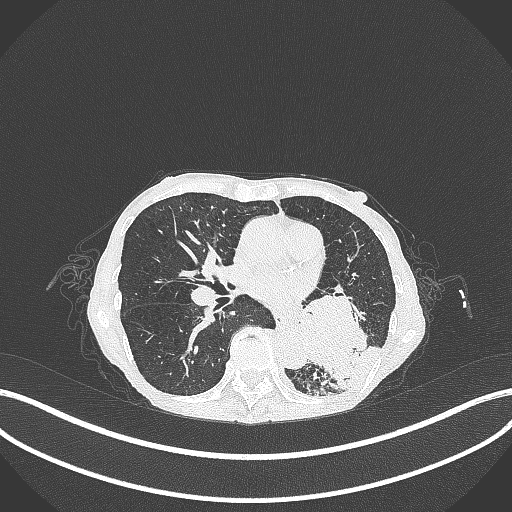
Chest CT, one axial slice; position 133 of 347 along the scan axis; lung window (W 1500 / L -600 HU); 512 × 512 image matrix, field of view 400 × 400 mm. Patient: female, 70 years. From the clinical record (not read from this slice): clinical TNM (as recorded): T3 N0 M0.
Outlined on this slice (rectangle marked by the reading radiologist):
- lung tumour (recorded histology: small cell carcinoma): box from (x=293, y=284) to (x=373, y=386) px